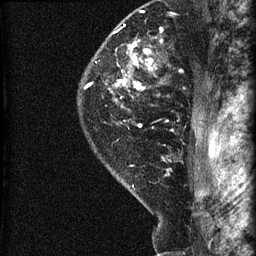
Breast MRI (dynamic contrast-enhanced), one sagittal slice; position 51 of 60 along the scan axis; dynamic contrast-enhanced series, image 2 of 3 at this slice position (ordered by acquisition); 1.5 T; TE 4.2 ms, TR 22.7 ms; 256 × 256 image matrix. Patient: female, 45 years. Case-level facts recorded for this patient, not image findings: setting: breast cancer imaged before/during neoadjuvant chemotherapy; receptor status: HR-positive, HER2-negative.
Outlined on this slice (semi-automatically segmented with operator editing):
- analysis volume of interest (the breast-tissue region the enhancement analysis was run in; not a lesion): bounding box <78,11,205,140> (left, top, right, bottom; pixels)
- tumour enhancement mask (voxels above the 90 % enhancement threshold inside the analysis volume of interest): <85,42,154,127>